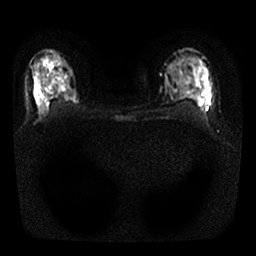
Breast MRI, one axial slice; position 16 of 25 along the scan axis; diffusion-weighted series; image 2 of 4 stored at this slice position (different b-values; order by instance number); 1.5 T; 4 mm slice thickness; 256 × 256 image matrix, field of view 300 × 300 mm. Female patient.
Outlined on this slice (expert manual segmentation):
- tumour on diffusion-weighted imaging: bounding box (x1, y1, x2, y2) in pixels: (35, 60, 76, 105)